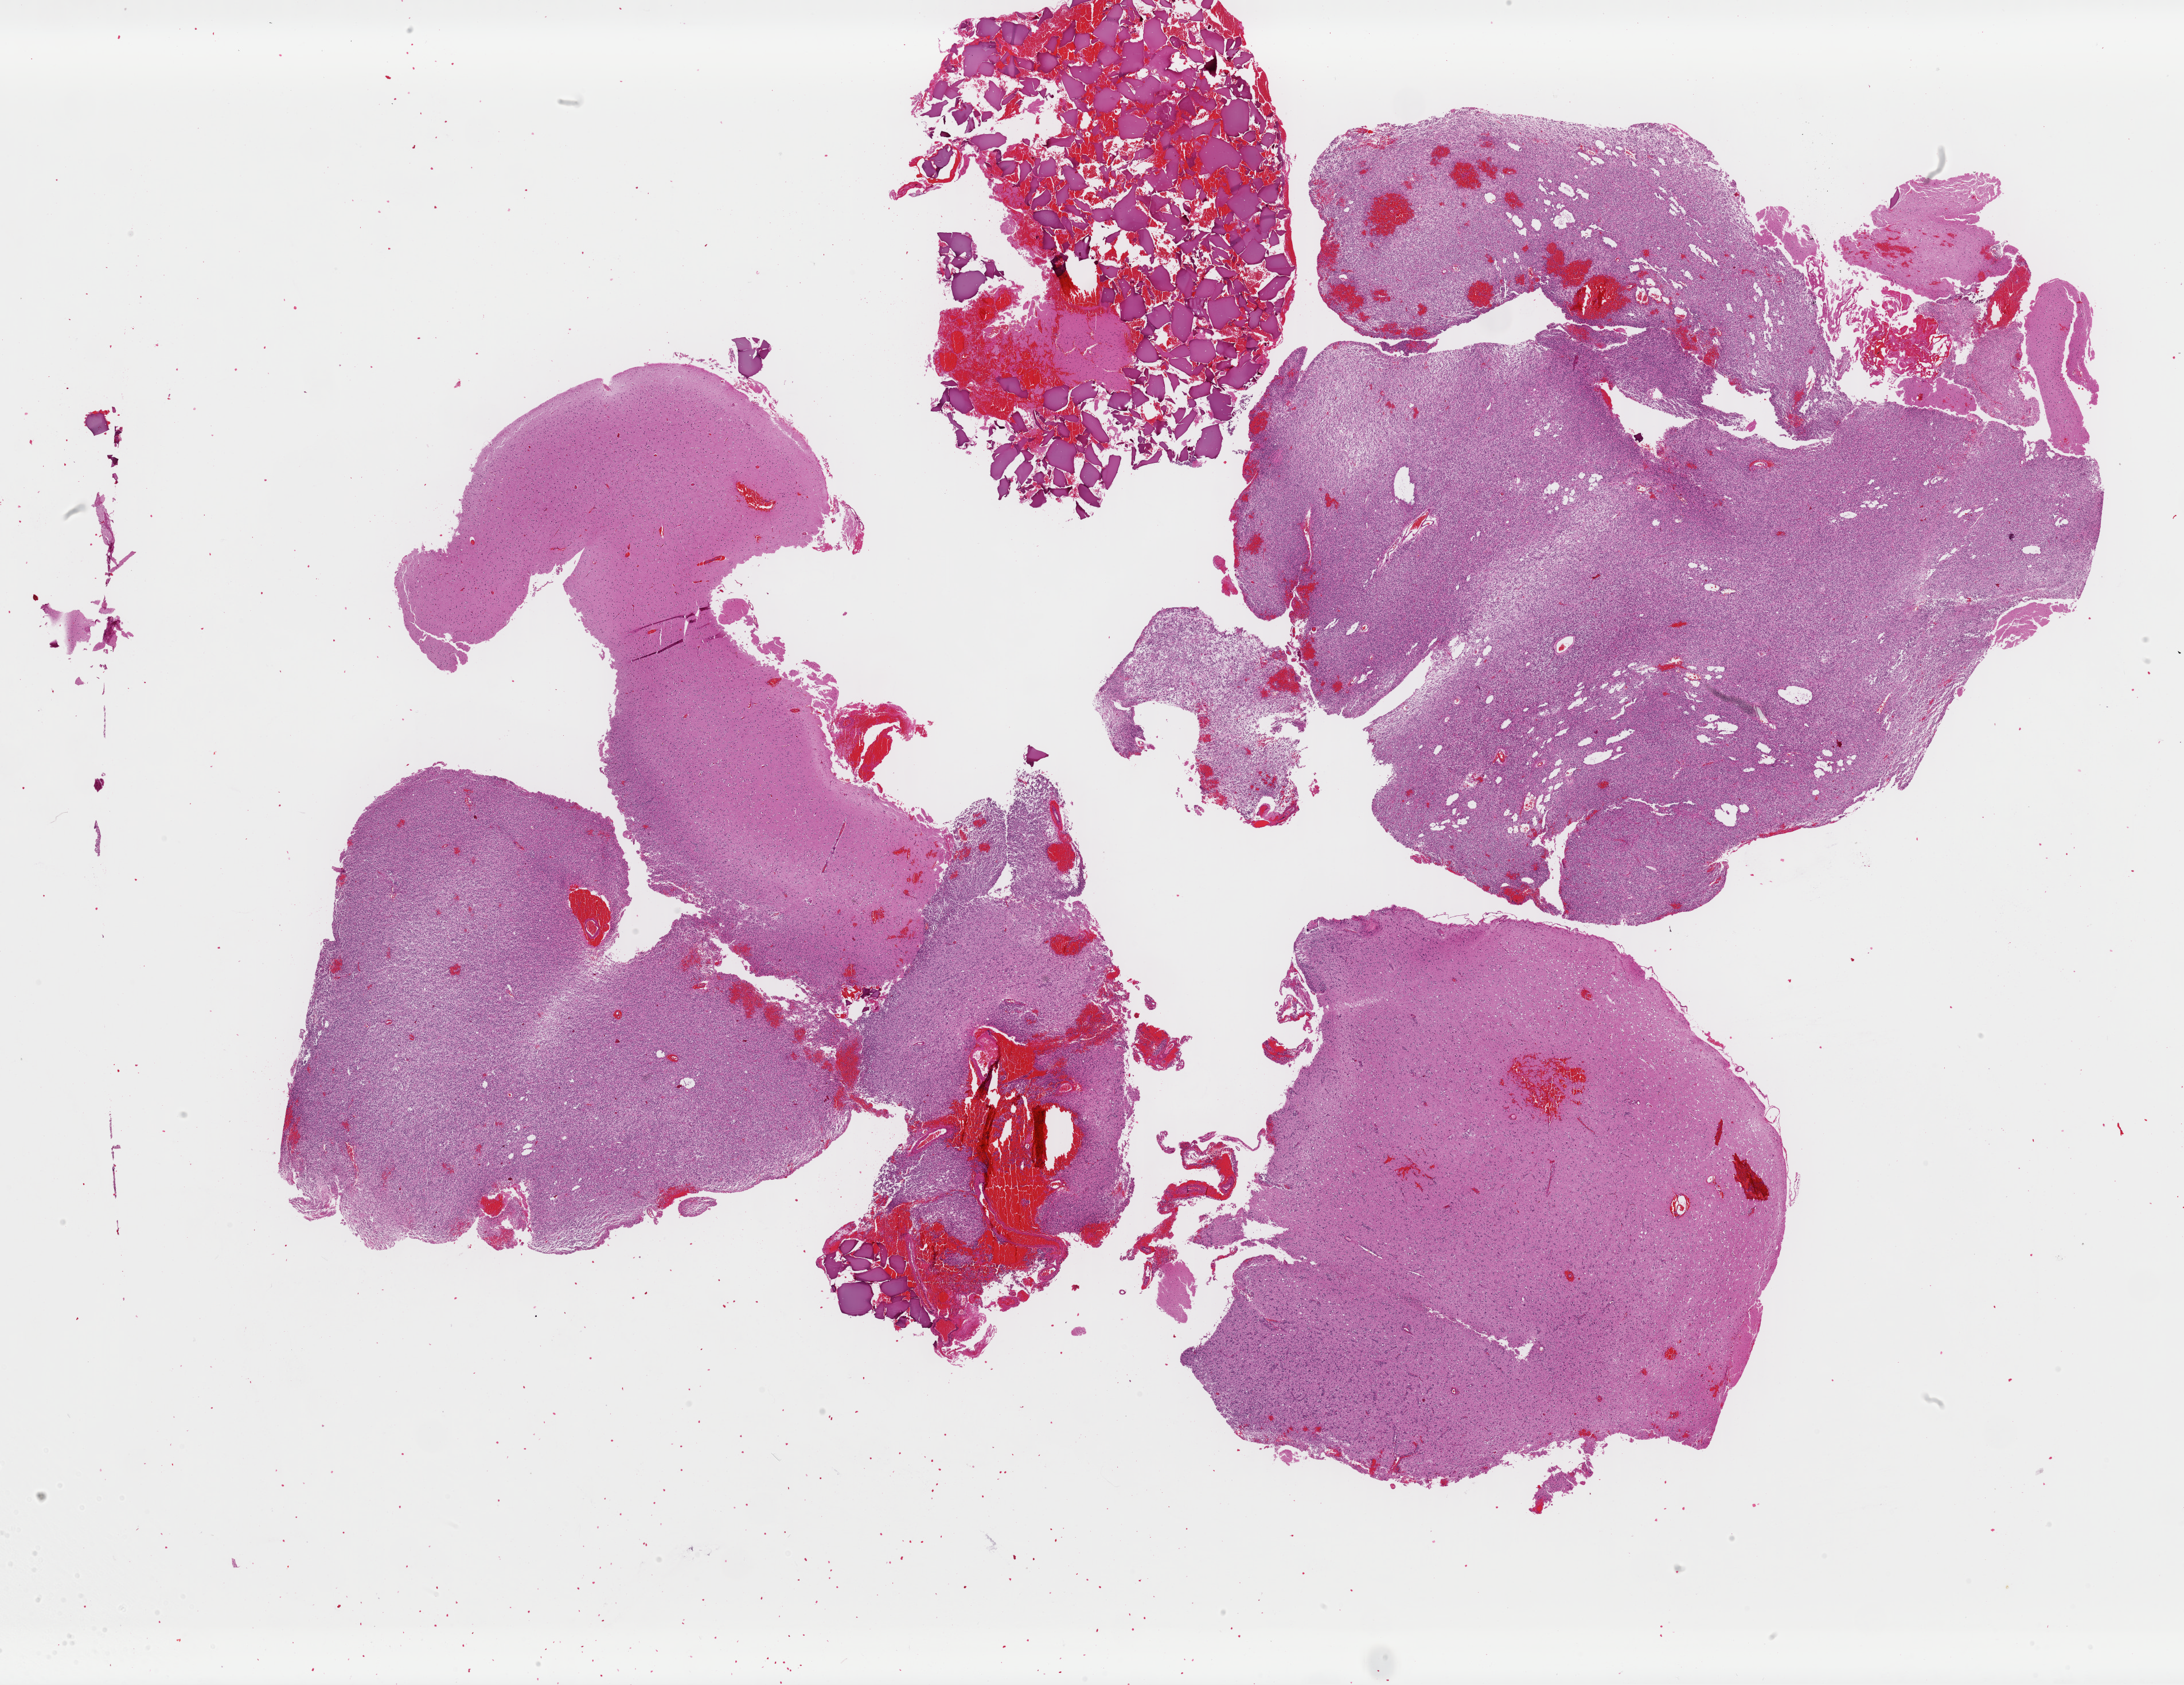
Digitized H&E tissue section (whole slide), shown as a low-resolution overview of the whole scanned area (about 30.1 x 23.2 mm). Formalin-fixed paraffin-embedded (FFPE) diagnostic section. Recurrent tumour sample from the brain. Patient: female, age at initial diagnosis 27 years.
This section: recurrent tumour. Patient diagnosis: Oligodendroglioma, NOS.